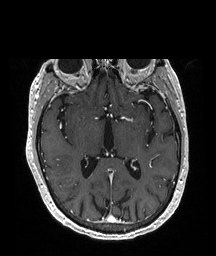
Brain MRI from a brain-tumour surgery series, one axial slice; position 112 of 208 along the scan axis; T1-weighted post-contrast; 216 × 256 image matrix. Case-level facts recorded for this patient, not image findings: histopathology: Glioblastoma; WHO grade: 4.
Structures marked on this image (expert manual segmentation):
- tumour: bounding box (x1, y1, x2, y2) in pixels: (63, 181, 75, 188)